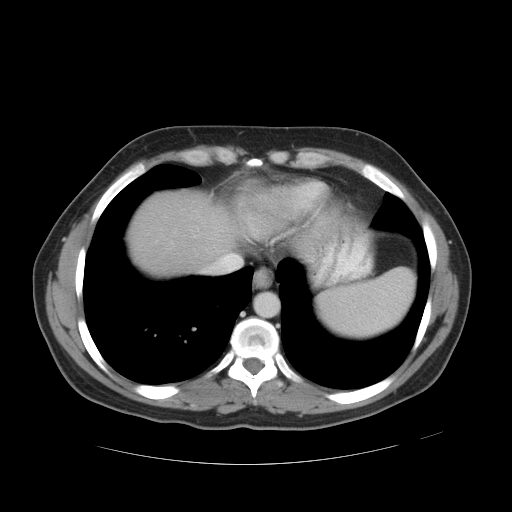
Contrast-enhanced abdominal CT, one axial slice; slice 45 of 49 in the series (ordered by position); reconstruction kernel STANDARD; intravenous contrast given; soft-tissue window (W 400 / L 40 HU); 512 × 512 image matrix, field of view 422 × 422 mm. Male patient, age 42 years. Case-level facts recorded for this patient, not image findings: diagnosis: colorectal cancer liver metastases, imaged before liver resection; multiple liver metastases: yes; largest metastasis: 2.8 cm; chemotherapy before resection: yes.
Outlined on this slice (manually delineated by an expert):
- hepatic veins: bounding box <204,250,243,273> (left, top, right, bottom; pixels)
- liver: <130,194,232,275>
- planned liver remnant (the part of the liver to remain after resection): <130,194,232,275>